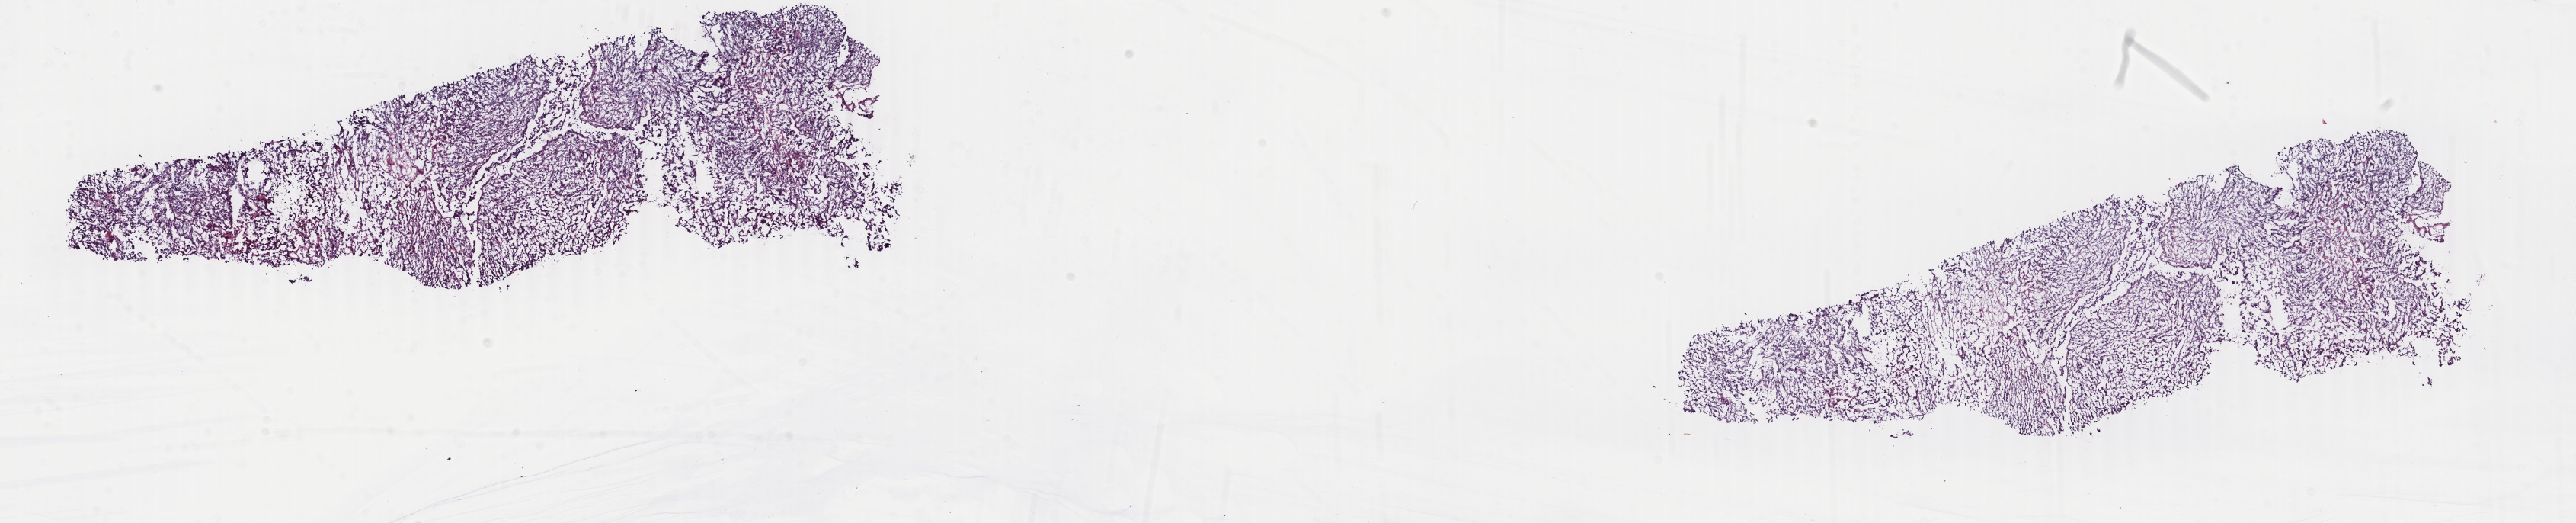
Digitized H&E tissue section (whole slide) — shown as a low-resolution overview of the whole scanned area (about 26.9 x 5.5 mm). Frozen section. Sample: primary tumour, uterus. Patient: female, age at initial diagnosis 69 years. Pathologist review of this section (percent, as recorded): tumour cells 90%, tumour nuclei 90%, normal cells 0%, stromal cells 5%, necrosis 5%. Inflammatory infiltration, as recorded: lymphocyte infiltration 40%, monocyte infiltration 20%, neutrophil infiltration 20%.
FIGO stage: IIIC1. Diagnosis: Mullerian mixed tumor.